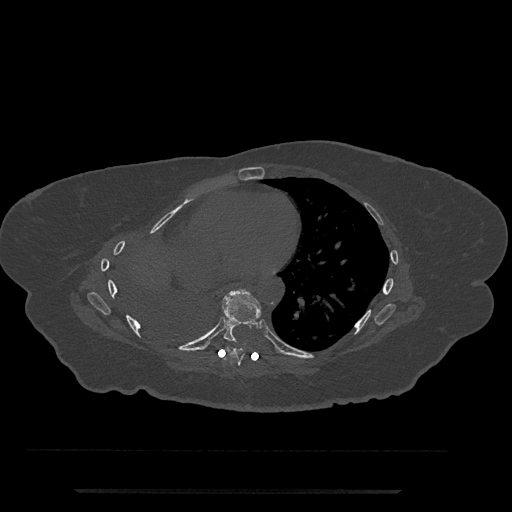
CT including the spine, one axial slice. Slice 416 of 797 in the series (ordered by position). Reconstruction kernel Br40s/3. 120 kVp. Bone window (W 1800 / L 400 HU). 512 × 512 image matrix. Patient: female, 51 years. Case-level facts recorded for this patient, not image findings: primary cancer: neuro.
Structures marked on this image (semi-automatic segmentation, software-assisted and operator-edited):
- T7 vertebra: box from (x=224, y=346) to (x=245, y=366) px
- T8 vertebra: (x=222, y=289)–(x=261, y=341)